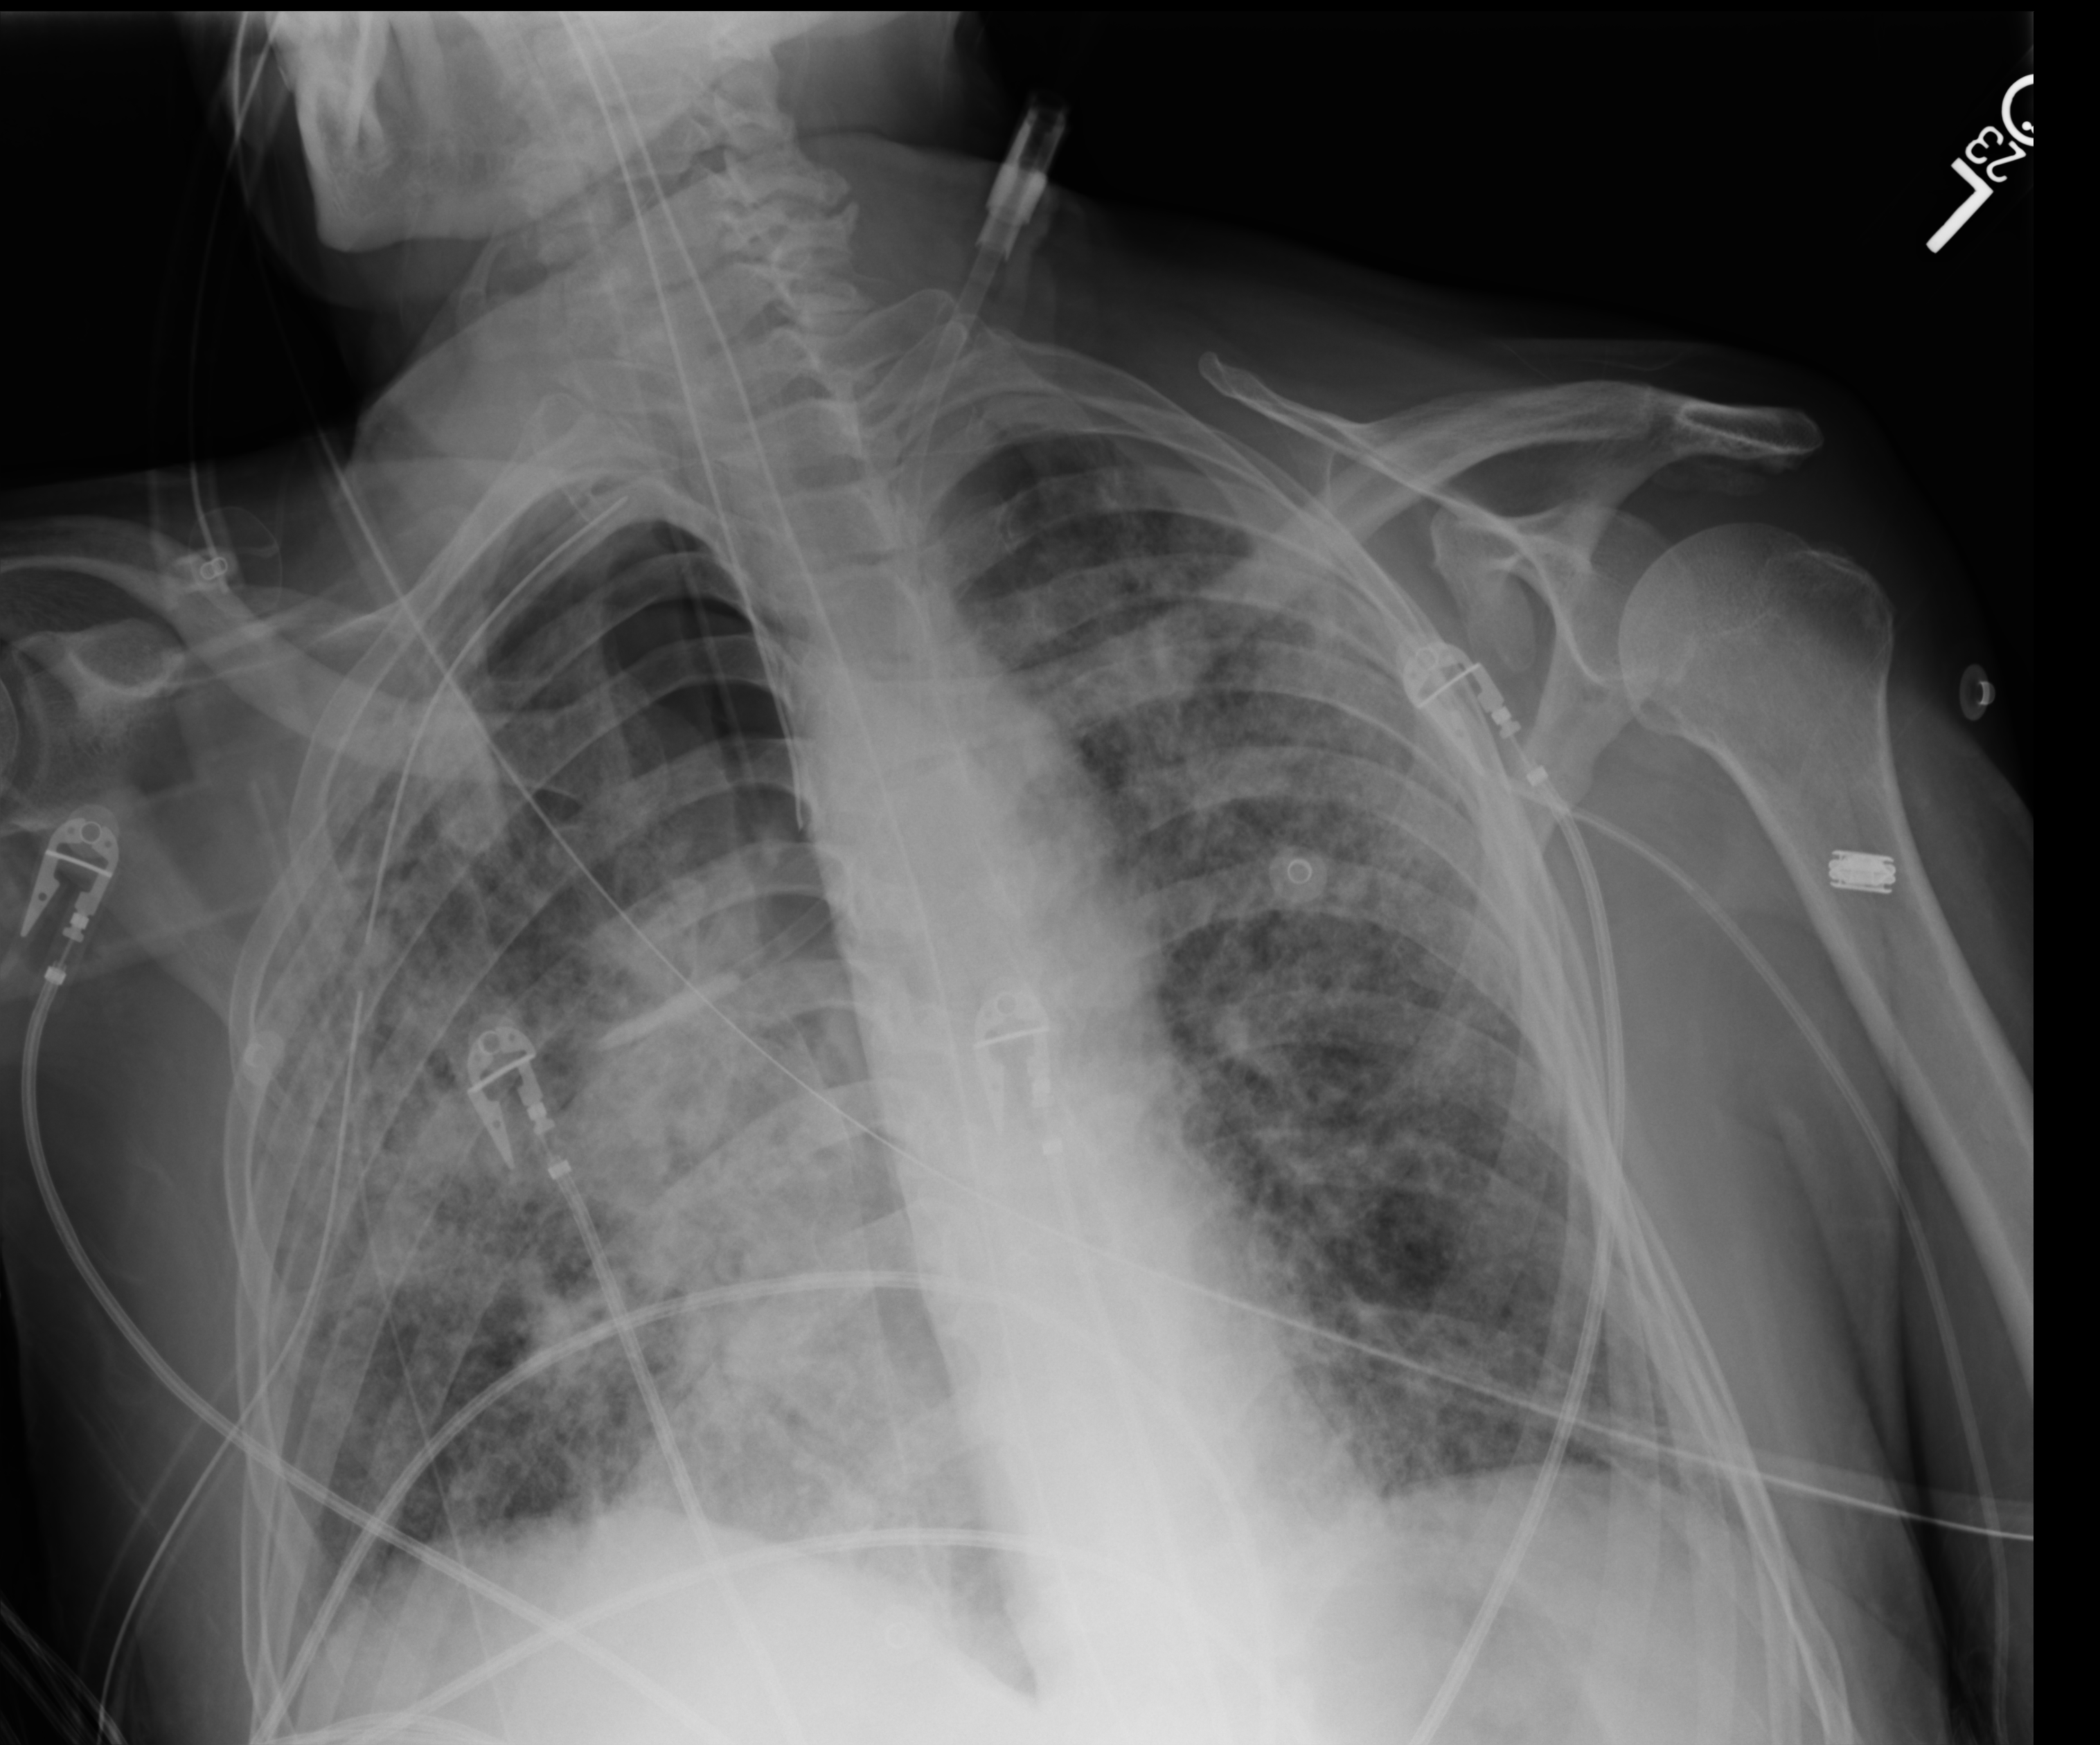
Chest X-ray (portable); anteroposterior (AP) projection. Male patient hospitalised with COVID-19, age 60–74 years.
Hospital-stay facts (about this admission, not read from this image; timing relative to this image not recorded):
- mechanically ventilated during this hospital stay: yes
- admitted to intensive care during this hospital stay: yes
- chronic kidney disease (admission record): no